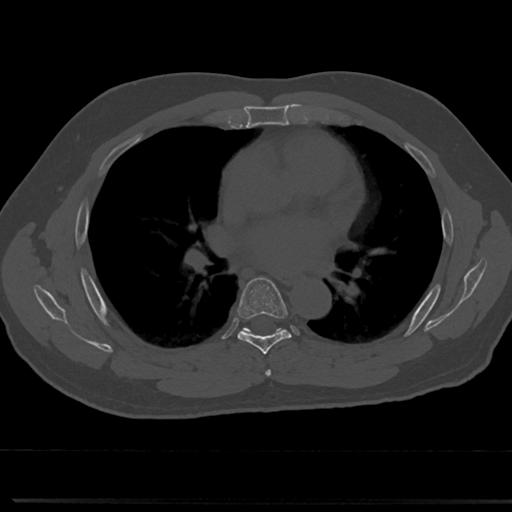
CT including the spine, one axial slice. Slice 447 of 817 in the series (ordered by position). 120 kVp. Bone window (W 1800 / L 400 HU). 0.5 mm slice thickness. 512 × 512 image matrix, field of view 355 × 355 mm. Male patient, age 61 years. Case-level facts recorded for this patient, not image findings: primary cancer: prostate.
Annotated regions visible in this slice (semi-automatically segmented with operator editing):
- T5 vertebra: bounding box (x1, y1, x2, y2) in pixels: (264, 350, 273, 376)
- T6 vertebra: (219, 277, 310, 354)